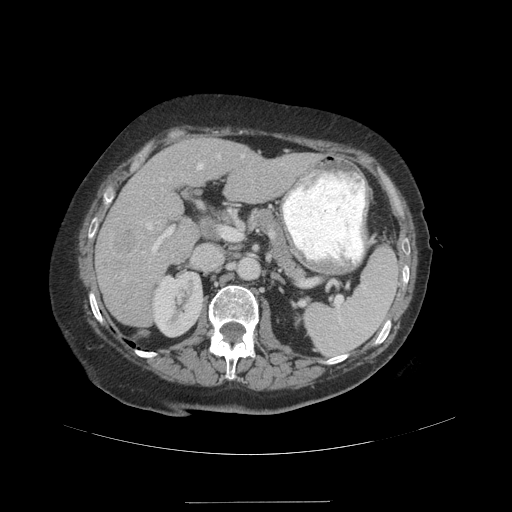
Contrast-enhanced abdominal CT (liver protocol), one axial slice. Slice 59 of 99 in the series (ordered by position). 140 kVp. Soft-tissue window (W 400 / L 40 HU). 2.5 mm slice thickness. 512 × 512 image matrix, field of view 440 × 440 mm. From the clinical record (not read from this slice): diagnosis: hepatocellular carcinoma (patient treated with transarterial chemoembolisation; whether this scan precedes or follows treatment is not stated here); TNM stage (as recorded): Stage-IVA.
Structures marked on this image (semi-automatic segmentation, software-assisted and operator-edited):
- liver parenchyma outside the tumour (the mass and vessels are separate outlines, so this box may not span the whole liver): bounding box (x1, y1, x2, y2) in pixels: (94, 138, 318, 326)
- mass: (114, 228, 137, 254)
- liver vessels: (146, 155, 244, 254)